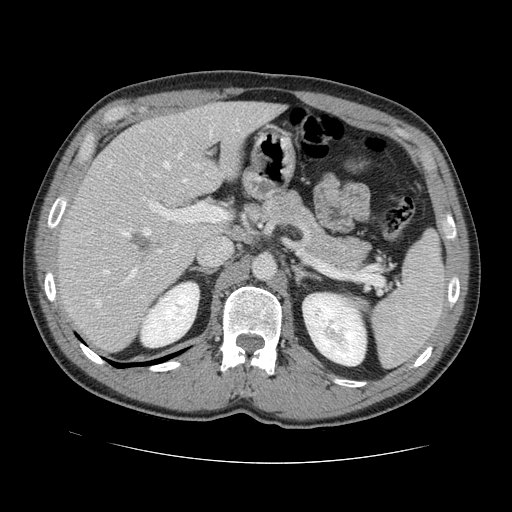
Contrast-enhanced abdominal CT, one axial slice. Intravenous contrast given. Soft-tissue window (W 400 / L 40 HU). 2.5 mm slice thickness. 512 × 512 image matrix, field of view 380 × 380 mm. Male patient, age 40 years. Case-level facts recorded for this patient, not image findings: diagnosis: colorectal cancer liver metastases, imaged before liver resection; multiple liver metastases: yes.
Annotated regions visible in this slice (expert manual segmentation):
- hepatic veins: bounding box [x1, y1, x2, y2] px = [96, 152, 187, 307]
- liver: [60, 102, 280, 352]
- planned liver remnant (the part of the liver to remain after resection): [103, 102, 281, 199]
- portal vein (with intrahepatic branches): [122, 172, 227, 284]
- liver metastasis: [131, 233, 155, 262]